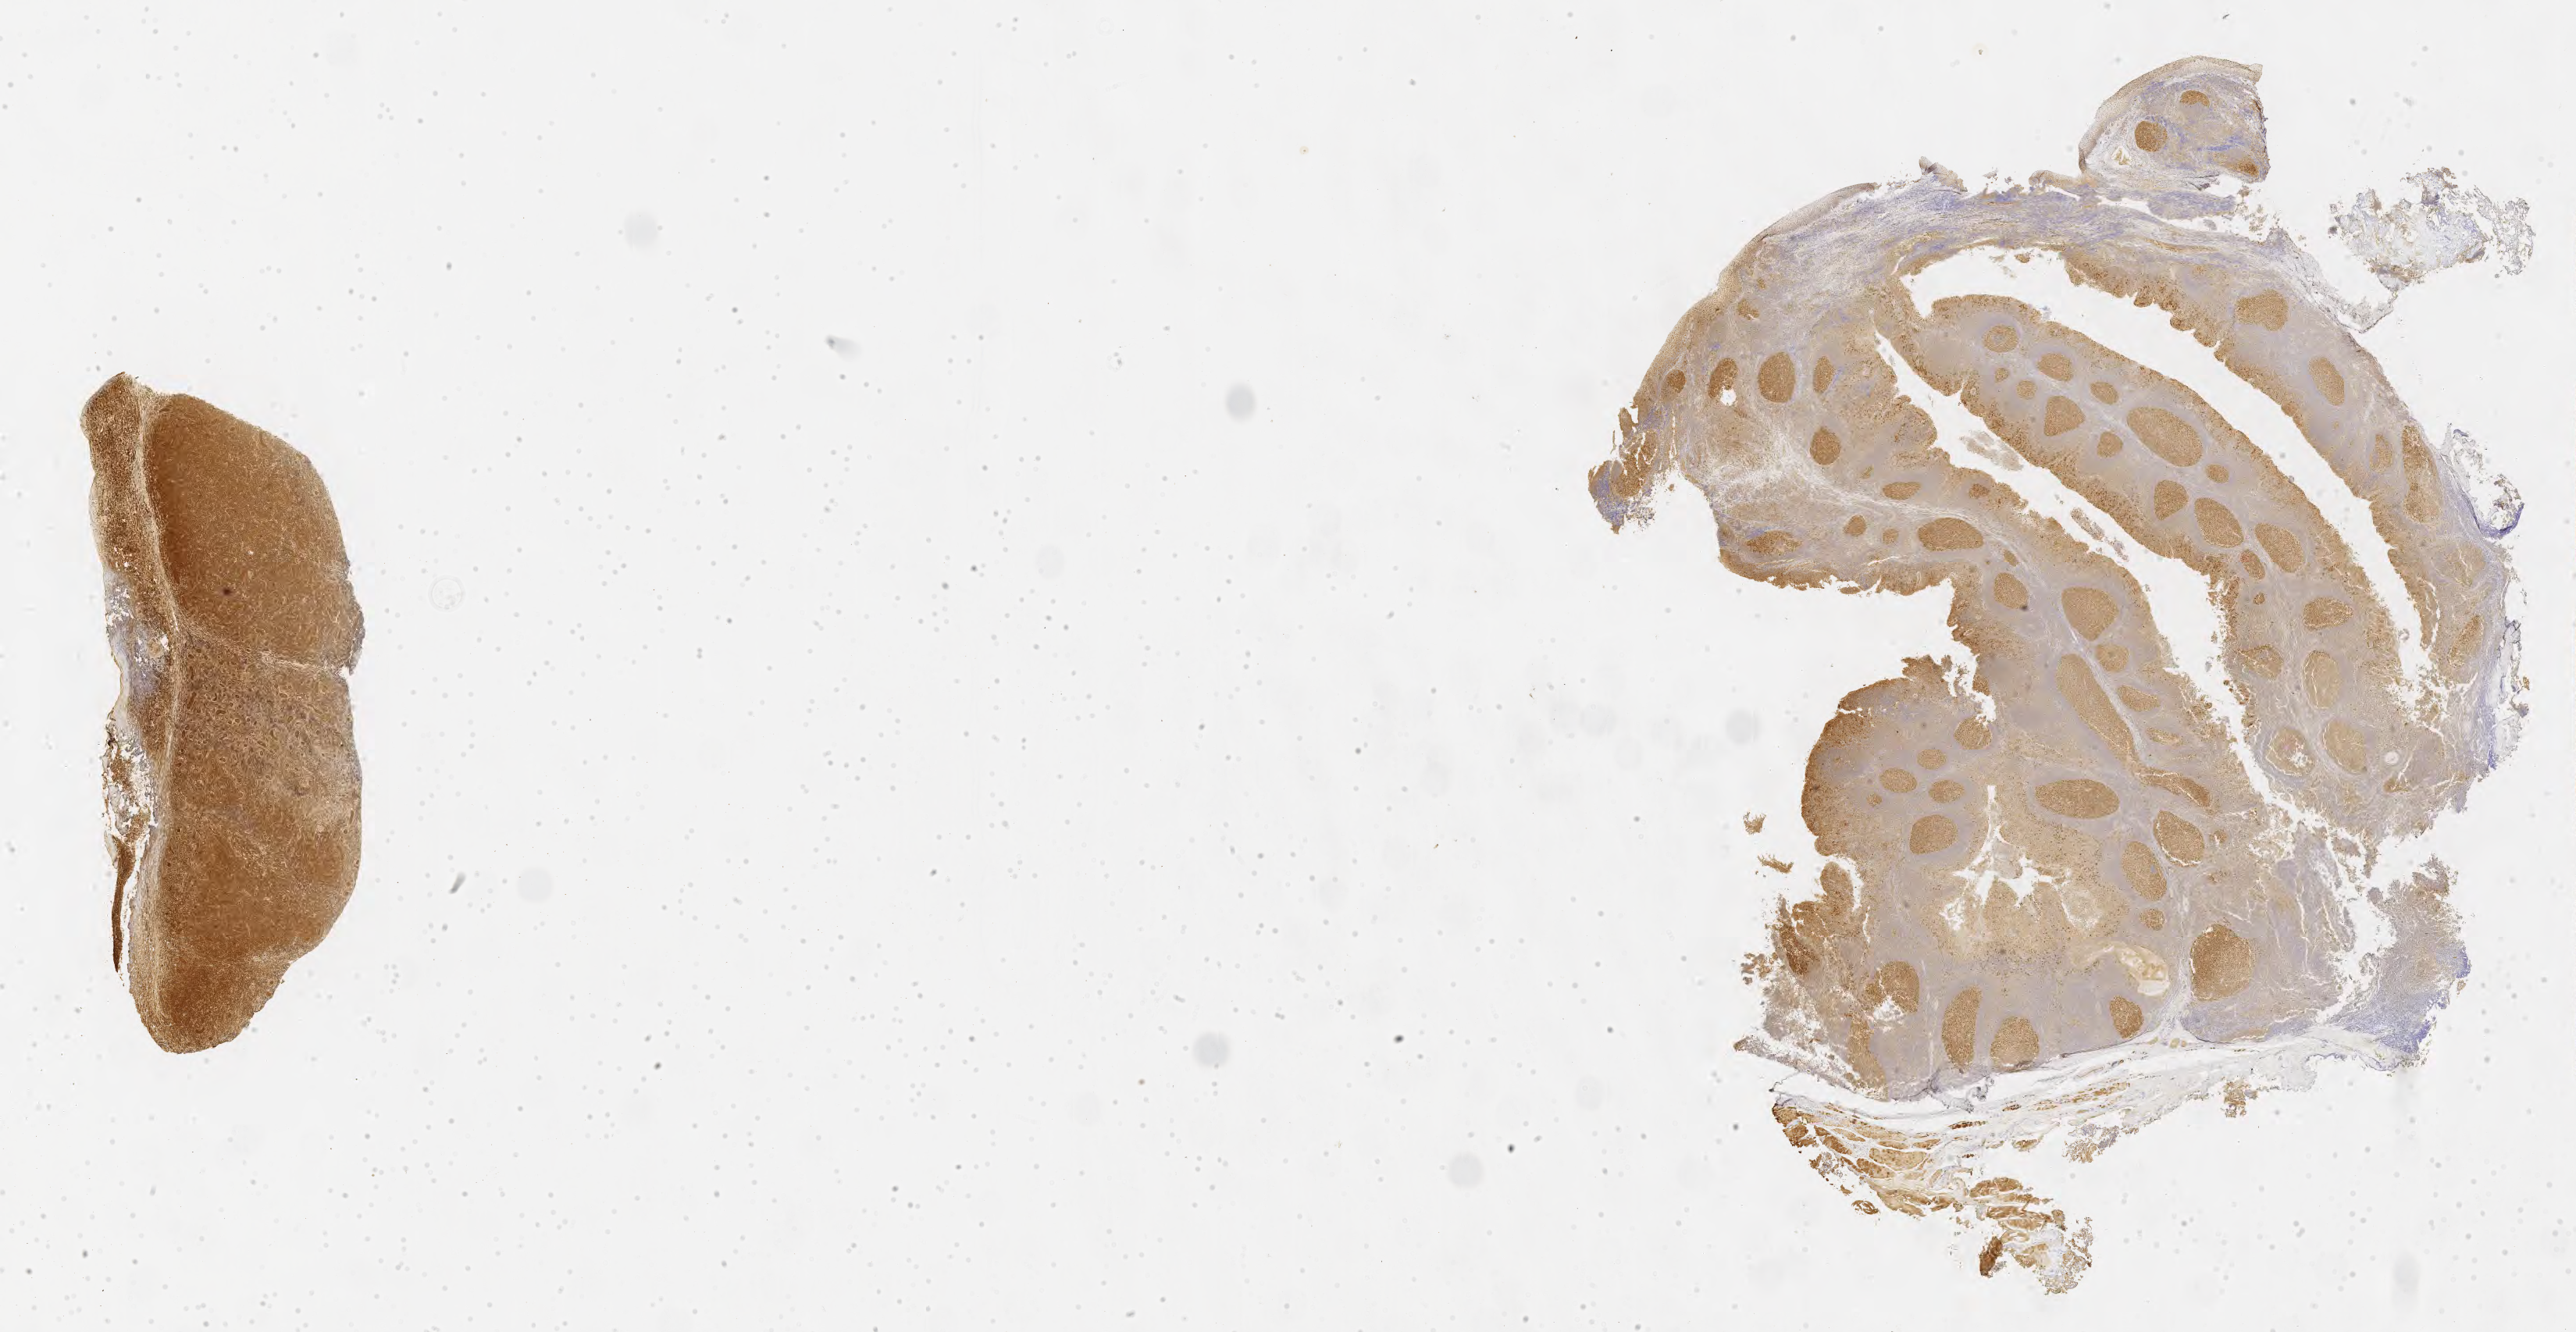
Immunohistochemistry (IHC) whole-slide image stained for BCL6 — shown as a low-resolution overview of the whole scanned area (about 26.7 x 13.8 mm), tumor tissue, site: testis. Male patient; age at initial diagnosis 8 years.
Diagnosis: Burkitt lymphoma, NOS.